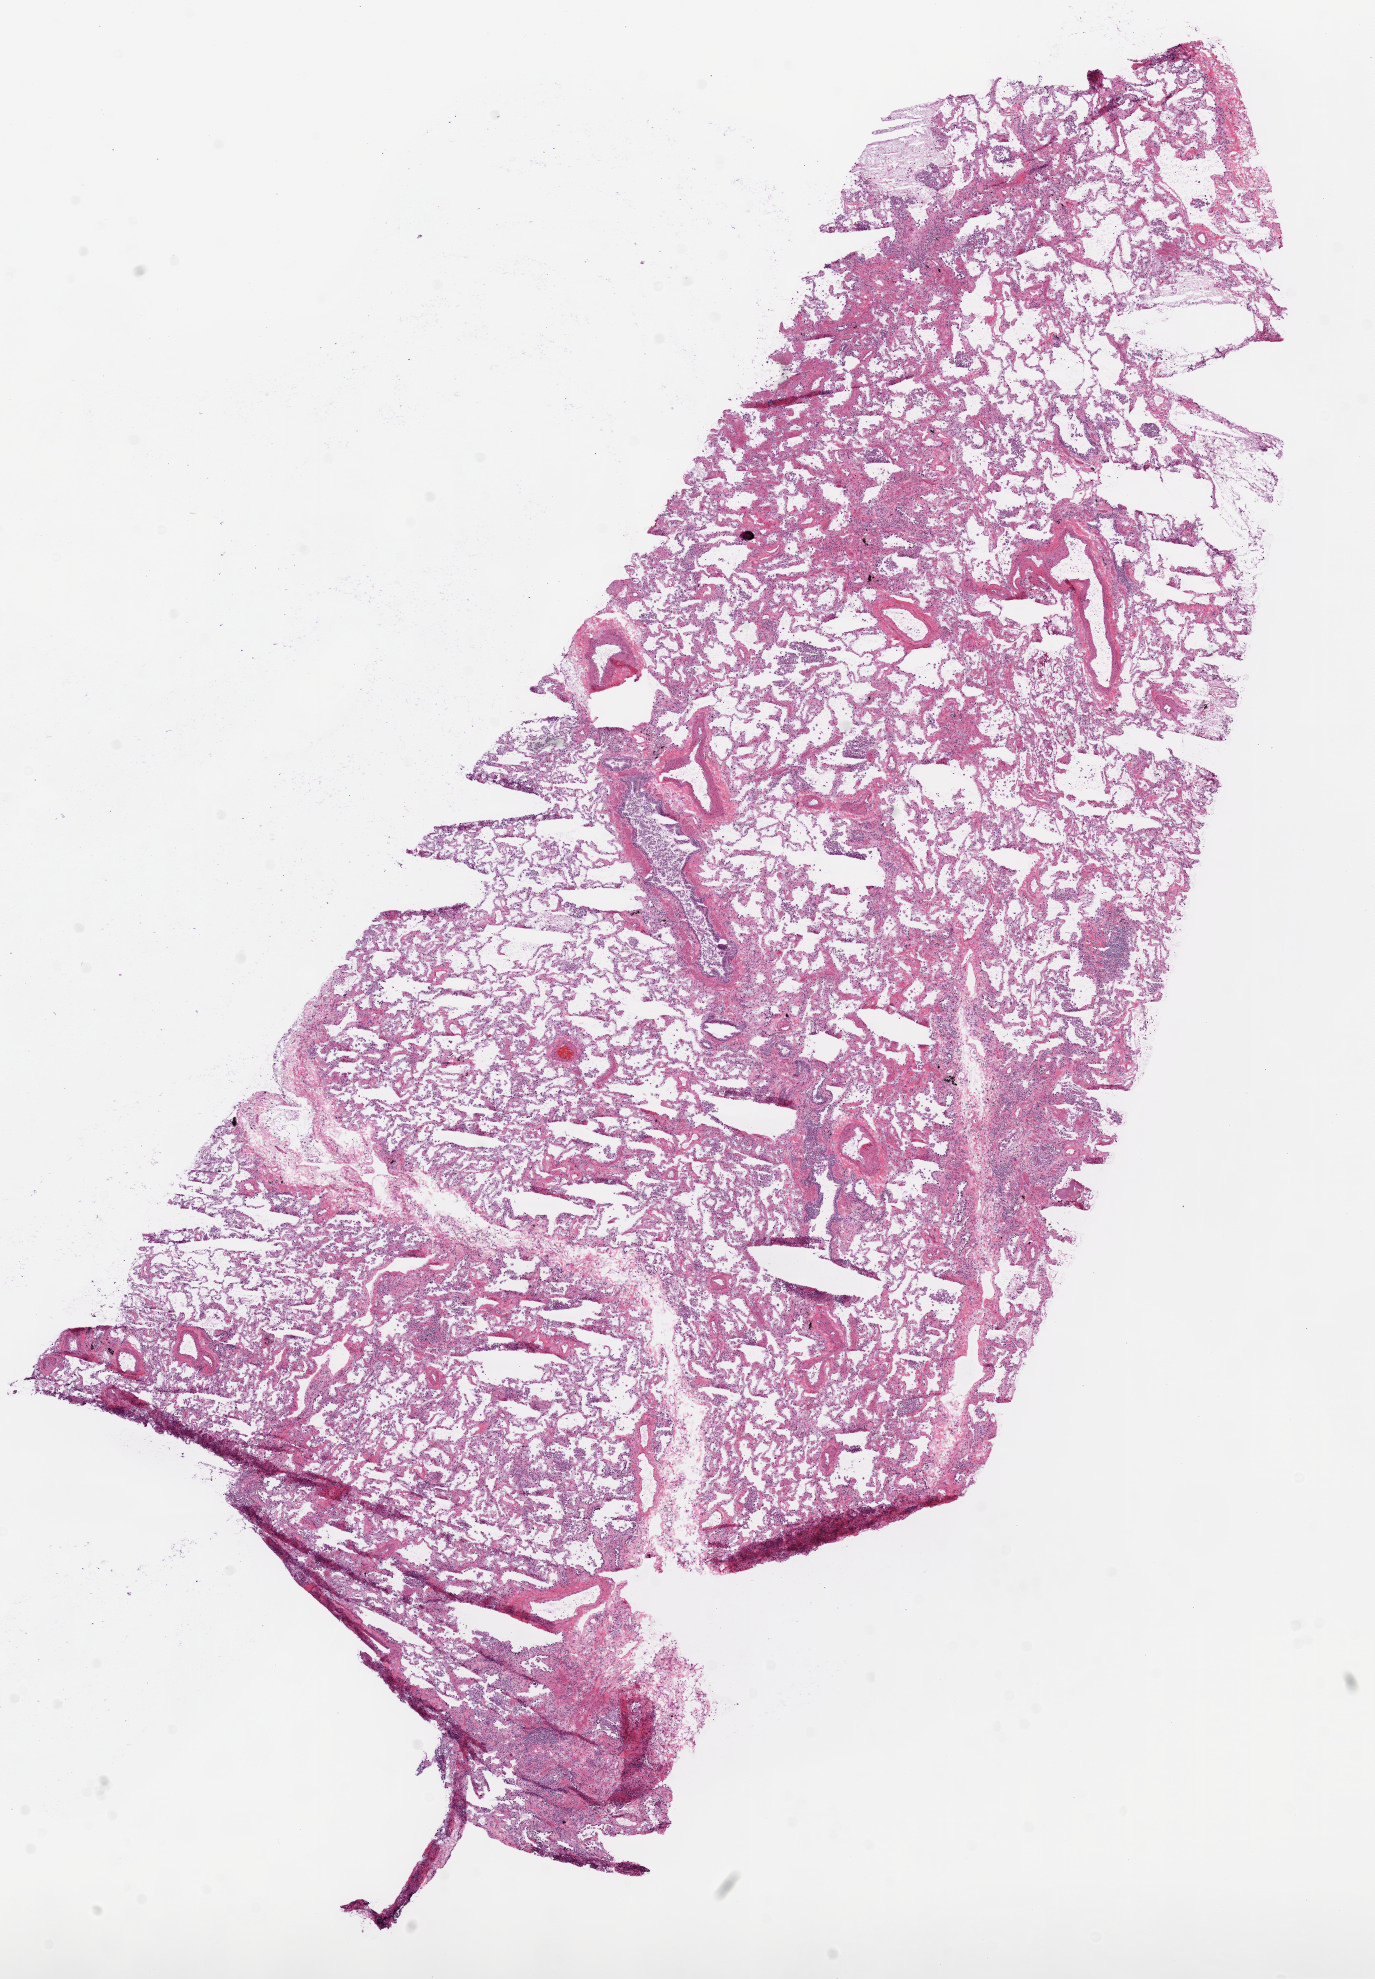
H&E-stained whole-slide image — shown as a low-resolution overview of the whole scanned area (about 11.0 x 15.9 mm, acquisition: 20x scan). Frozen section from the top of the tissue portion. Solid tissue normal (non-tumour tissue) sample from the lung. Patient: female, age at initial diagnosis 60 years.
This section: solid tissue normal sample (biorepository sample class). Patient diagnosis: Adenocarcinoma, NOS (upper lobe, lung).